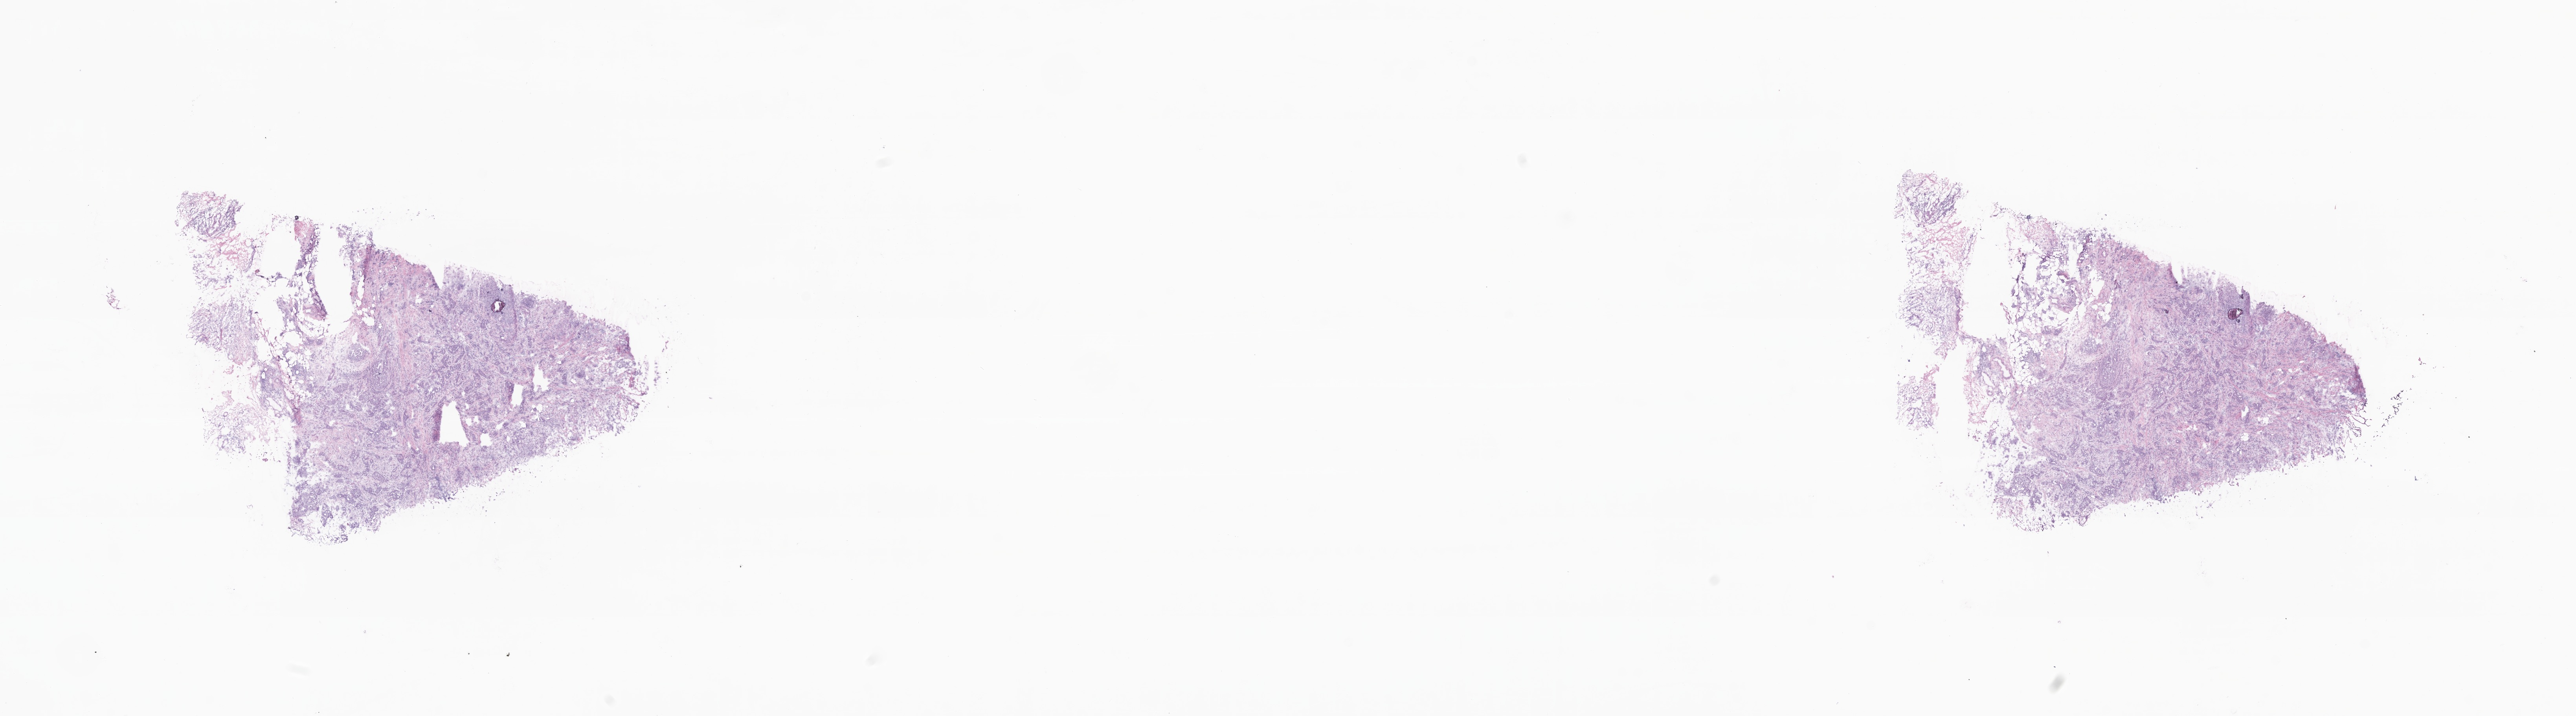
Whole-slide image, H&E stain, low-resolution overview of the scanned area, about 27.6 x 7.7 mm, frozen section (tissue freezing medium), primary tumor, site: breast (right). Female, age 41 years at initial diagnosis. Slide review estimates, as recorded: tumor cells 50%, tumor nuclei 80%, stromal cells 40%, necrosis 0%, normal cells 10%. Infiltration values recorded for this section: lymphocyte infiltration 0%, monocyte infiltration 0%, neutrophil infiltration 0%.
- histologic diagnosis: Infiltrating duct carcinoma, NOS